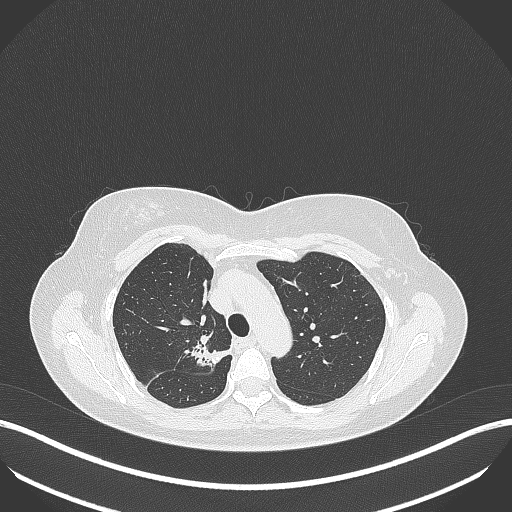
Chest CT, one axial slice. Slice 289 of 386 in the series (ordered by position). Reconstruction kernel B70f. Lung window (W 1500 / L -600 HU). 1 mm slice thickness. 512 × 512 image matrix, field of view 400 × 400 mm. Female patient, age 65 years. From the clinical record (not read from this slice): clinical TNM (as recorded): T1b N0 M0.
Outlined on this slice (rectangle marked by the reading radiologist):
- lung tumour (recorded histology: adenocarcinoma): bounding box [x1, y1, x2, y2] px = [186, 336, 230, 374]